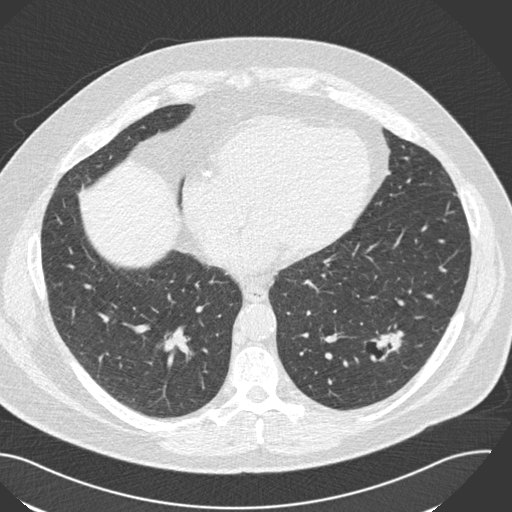
Low-dose screening chest CT, one axial slice. Position 67 of 153 along the scan axis. Reconstruction kernel B30f. 120 kVp. Lung window (W 1500 / L -600 HU). 2 mm slice thickness. 512 × 512 image matrix, field of view 394 × 394 mm.
Outlined on this slice (manually delineated by an expert):
- lesion 1 (tumor, lower lobe of left lung): bounding box <371,331,403,353> (left, top, right, bottom; pixels)